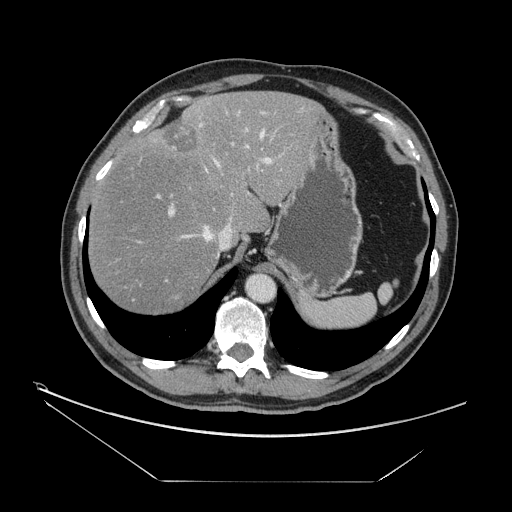
Contrast-enhanced abdominal CT, one axial slice; slice 117 of 161 in the series (ordered by position); reconstruction kernel STANDARD; intravenous contrast given; soft-tissue window (W 400 / L 40 HU); 2.5 mm slice thickness; 512 × 512 image matrix, field of view 440 × 440 mm. Male patient, age 65 years. Case-level facts recorded for this patient, not image findings: diagnosis: colorectal cancer liver metastases, imaged before liver resection; multiple liver metastases: yes; largest metastasis: 4.2 cm; chemotherapy before resection: yes.
Annotated regions visible in this slice (outlined manually by an expert reader):
- hepatic veins: box from (x=179, y=131) to (x=264, y=258) px
- liver: (x=89, y=92)–(x=322, y=315)
- planned liver remnant (the part of the liver to remain after resection): (x=89, y=92)–(x=320, y=315)
- portal vein (with intrahepatic branches): (x=156, y=107)–(x=305, y=217)
- liver metastasis: (x=160, y=118)–(x=196, y=154)